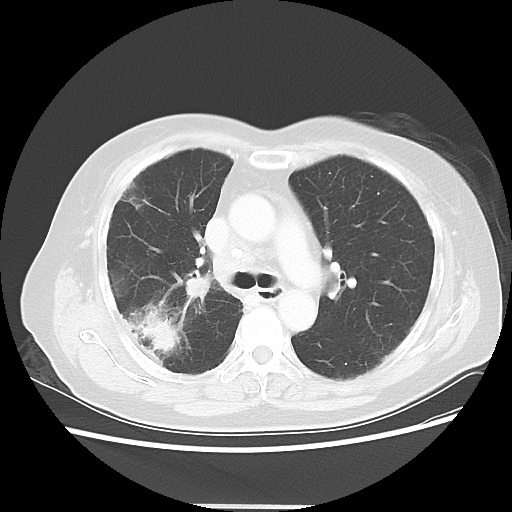
Chest CT, one axial slice. Slice 31 of 50 in the series (ordered by position). Lung window (W 1500 / L -600 HU). 5 mm slice thickness. 512 × 512 image matrix, field of view 360 × 360 mm. Female patient, age 72 years. Case-level facts recorded for this patient, not image findings: clinical TNM (as recorded): T2 N1 M0; histopathological grade: G1.
Outlined on this slice (bounding box drawn by a radiologist):
- lung tumour (recorded histology: adenocarcinoma): bounding box <130,307,180,352> (left, top, right, bottom; pixels)